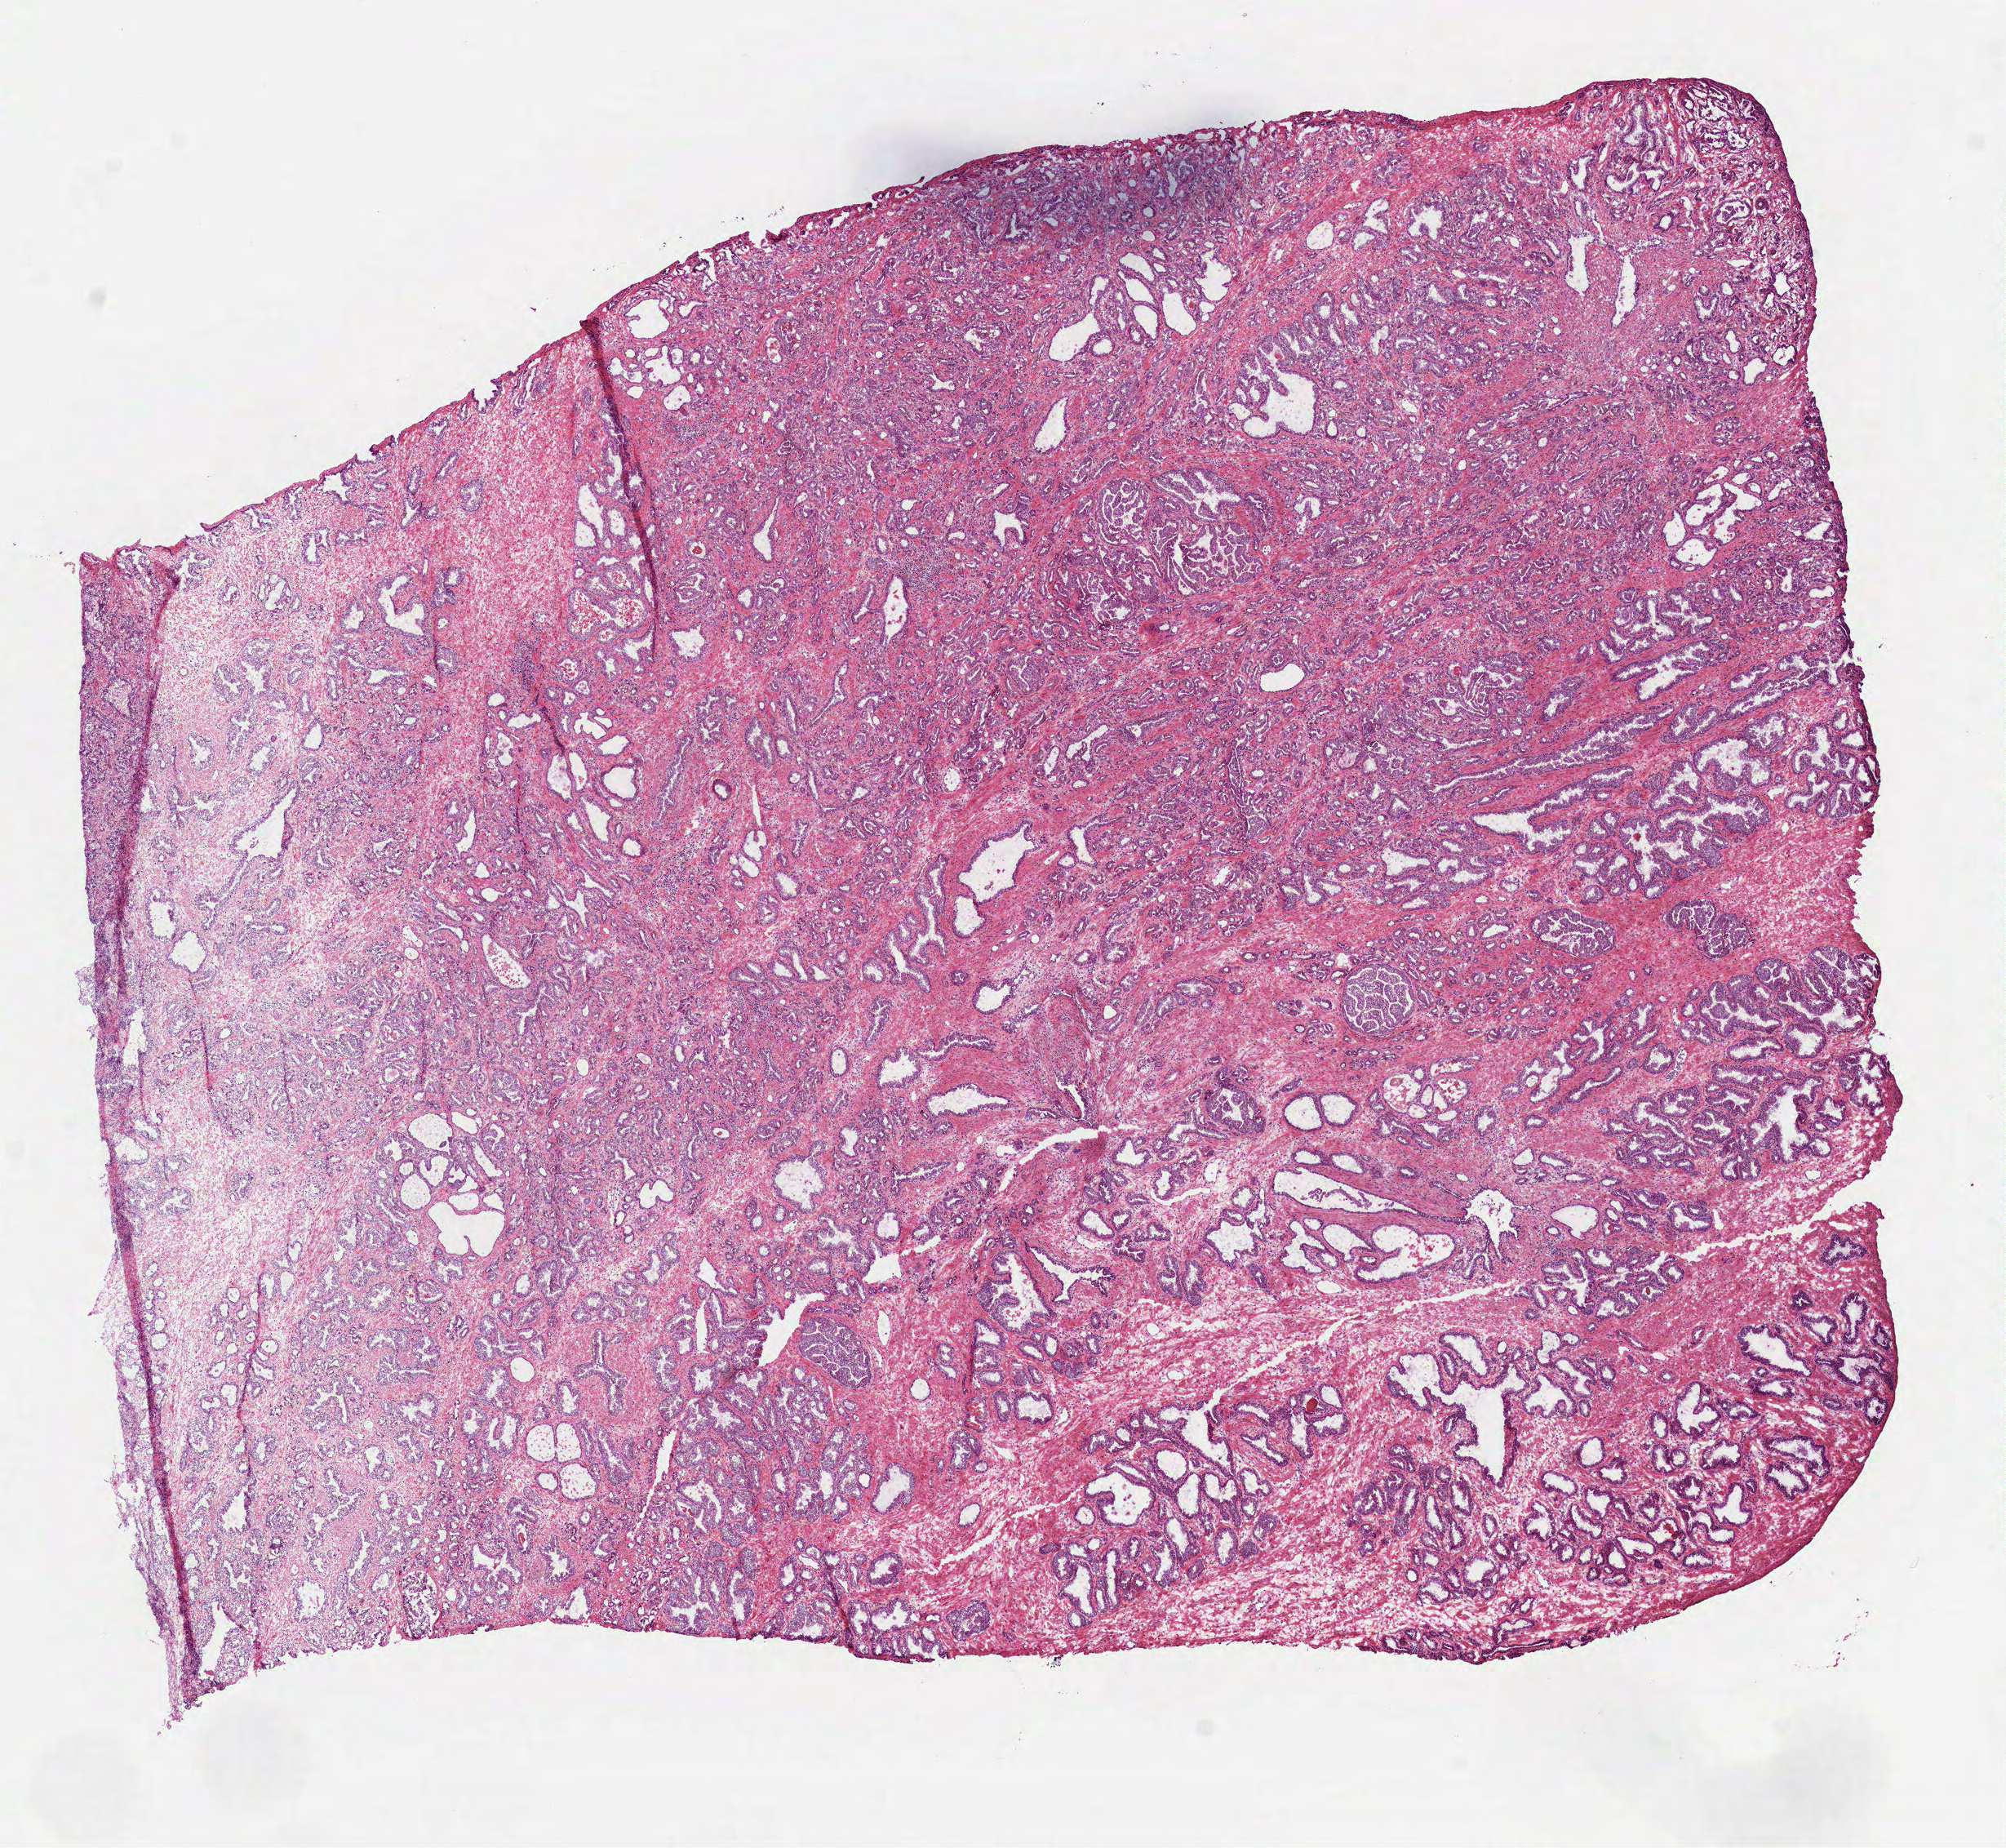
Hematoxylin and eosin (H&E) stained whole-slide image, shown as a low-resolution overview of the whole scanned area (about 9.9 x 9.1 mm, acquisition: 40x scan); frozen section from the bottom of the tissue portion; sample: primary tumour, prostate. Patient: male, age at initial diagnosis 52 years. Gleason score: 7 (4+3). Composition of this section per pathologist review: tumour cells 60%, tumour nuclei 60%, normal cells 25%, stromal cells 15%, necrosis 0%.
Lymph nodes positive (case pathology): 0 of 4 examined. Laterality: bilateral. Pathologic diagnosis: Acinar cell carcinoma (prostate gland).